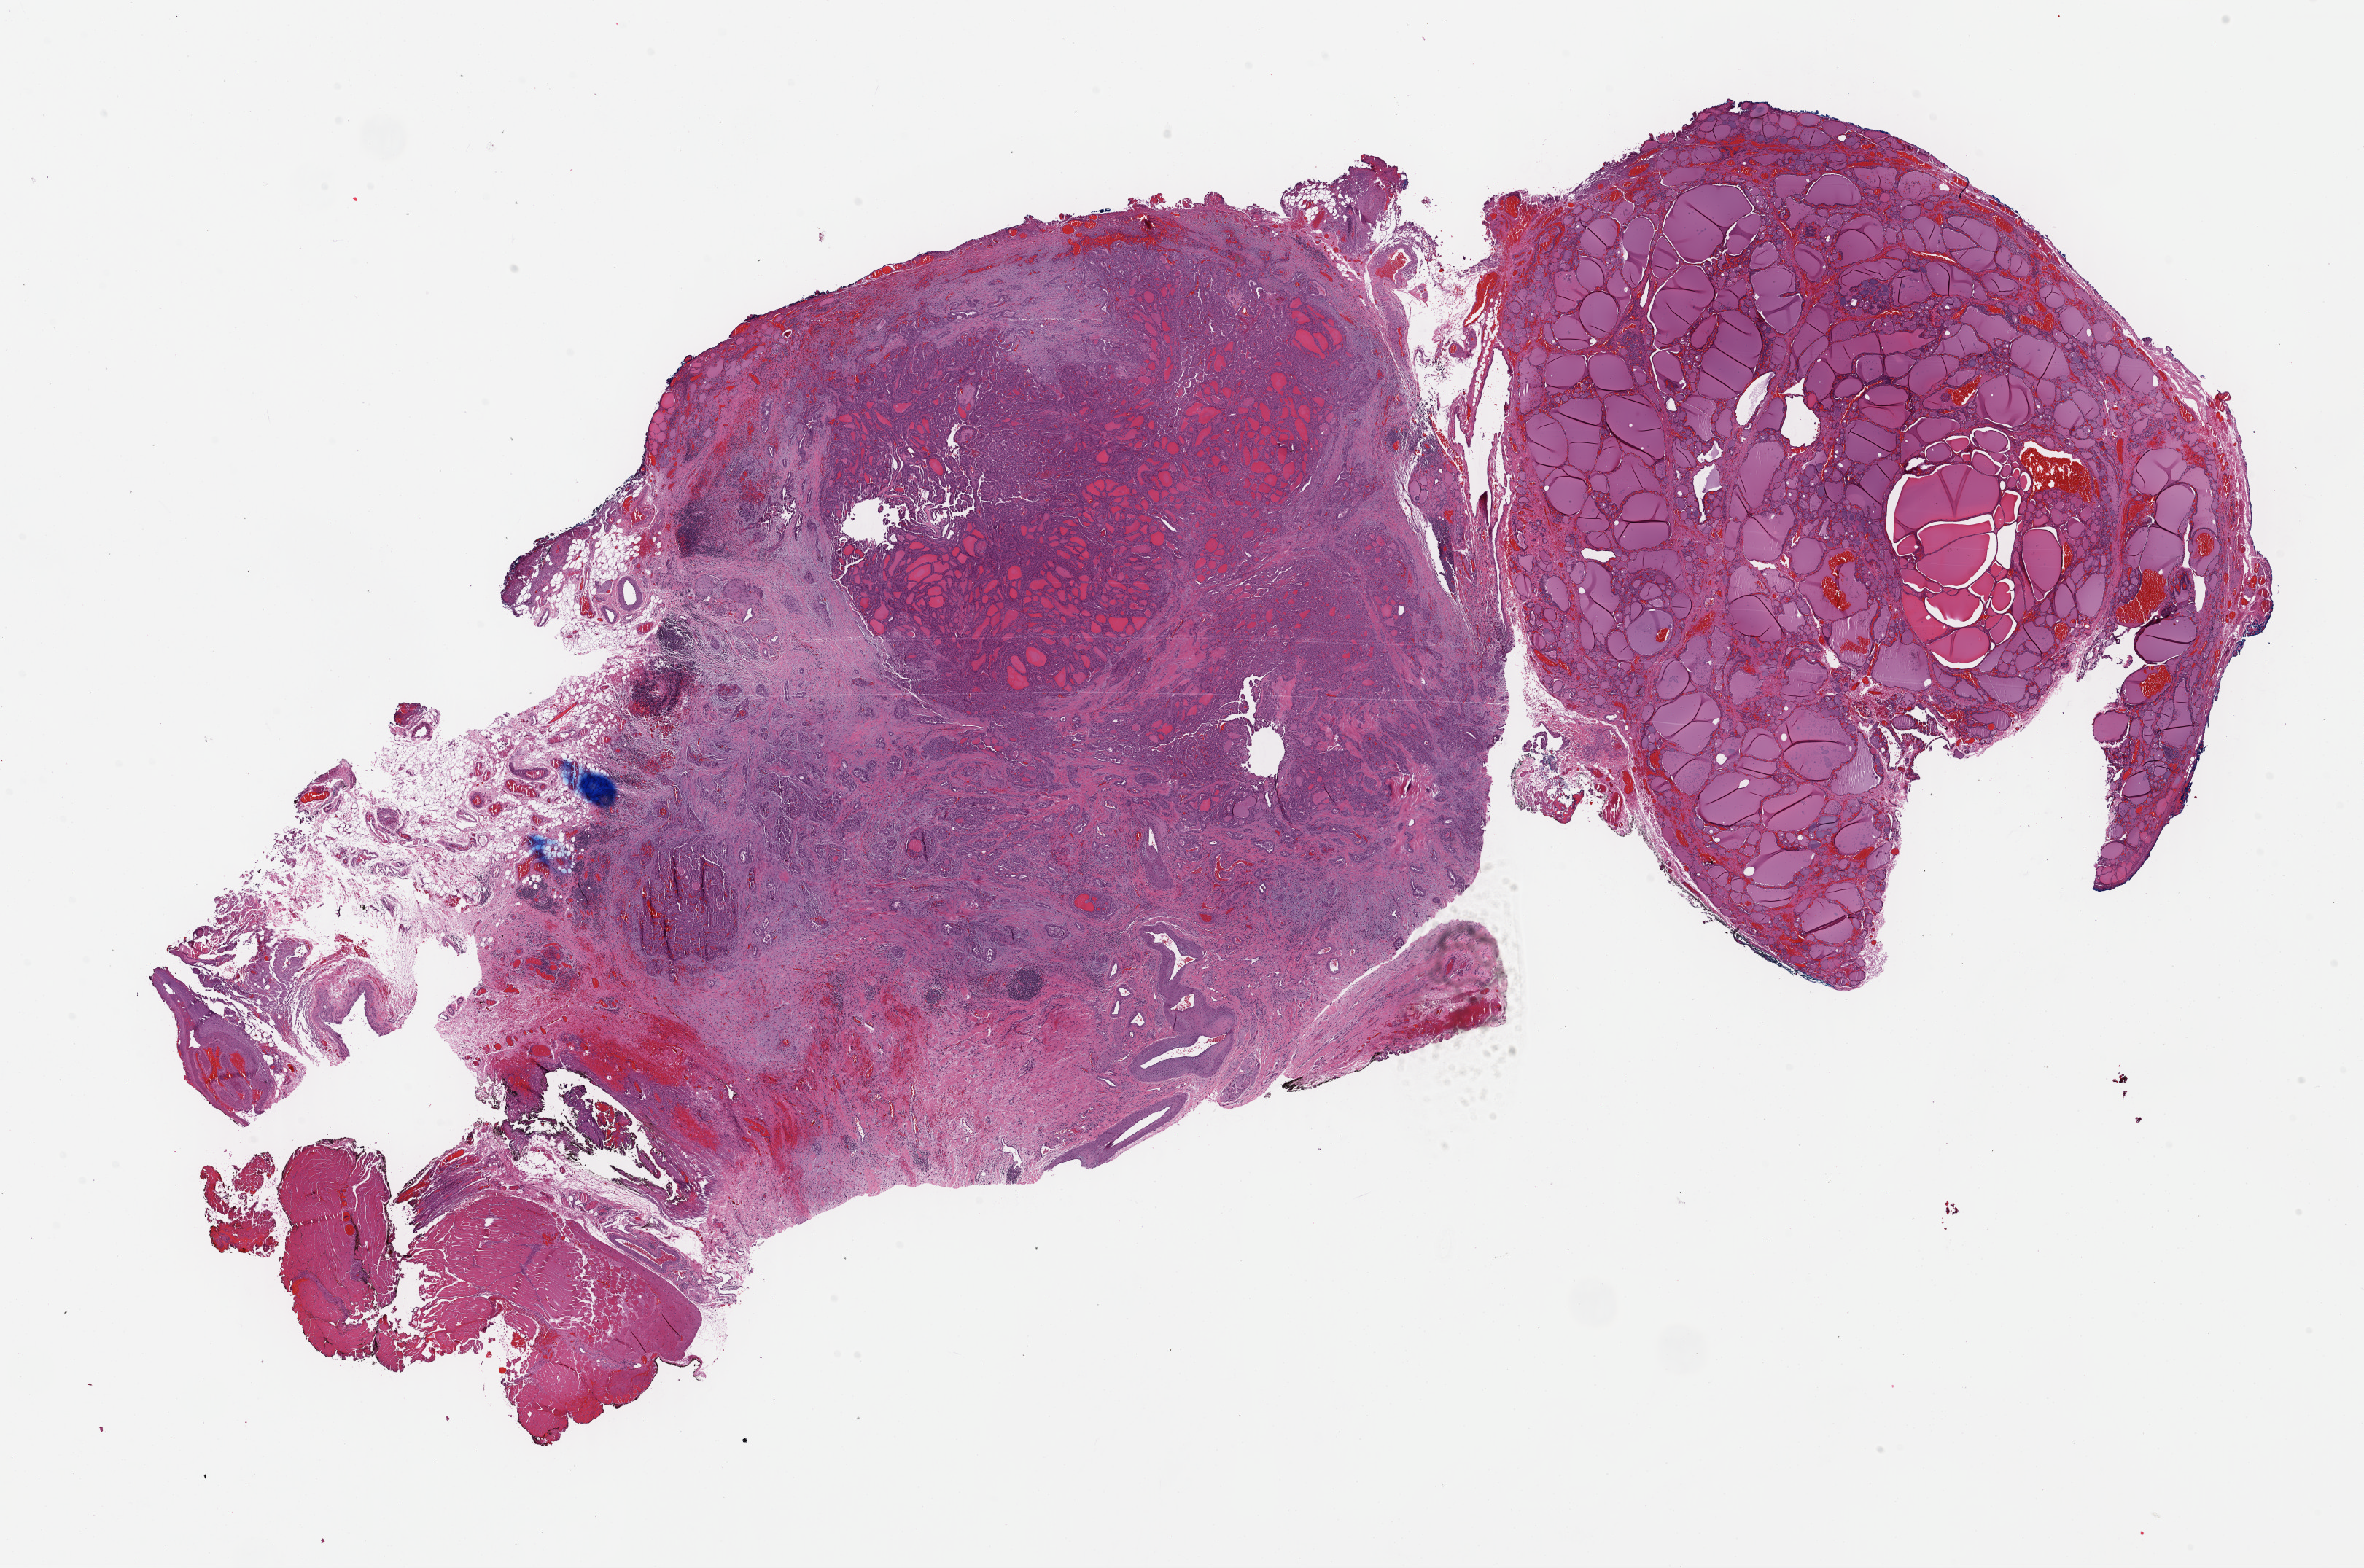
Whole-slide histology image, H&E, whole scanned area (about 25.5 x 16.9 mm) shown as a low-resolution overview, formalin-fixed paraffin-embedded (FFPE) diagnostic section, thyroid, primary tumour sample. Female, age 70 years at initial diagnosis.
- TNM: T3 N0 M0
- AJCC pathologic stage: III
- pathologic diagnosis: Papillary adenocarcinoma, NOS (thyroid gland)
- lymph nodes positive (case pathology): 0 of 15 examined